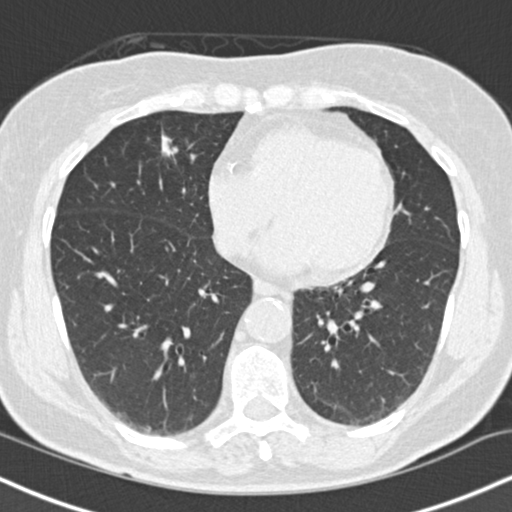
Chest CT (low-dose screening protocol), one axial image. Baseline annual screen. Lung window (W 1500 / L -600 HU). 2 mm slice thickness. Standard (soft-tissue) reconstruction kernel (B30f). Female, age 66 years at enrolment.
Lesion marked by an expert reader, bounding box [x1, y1, x2, y2] px = [141, 125, 187, 168]. Screening reader's record for this exam (one nodule recorded; not confirmed to be the boxed lesion): non-calcified nodule or mass ≥4 mm, right lower lobe, 10 × 8 mm, smooth margins, soft tissue attenuation. Official screen result: positive, change unspecified: nodule(s) >= 4 mm or enlarging nodule(s), mass(es), or other non-specific abnormalities suspicious for lung cancer.